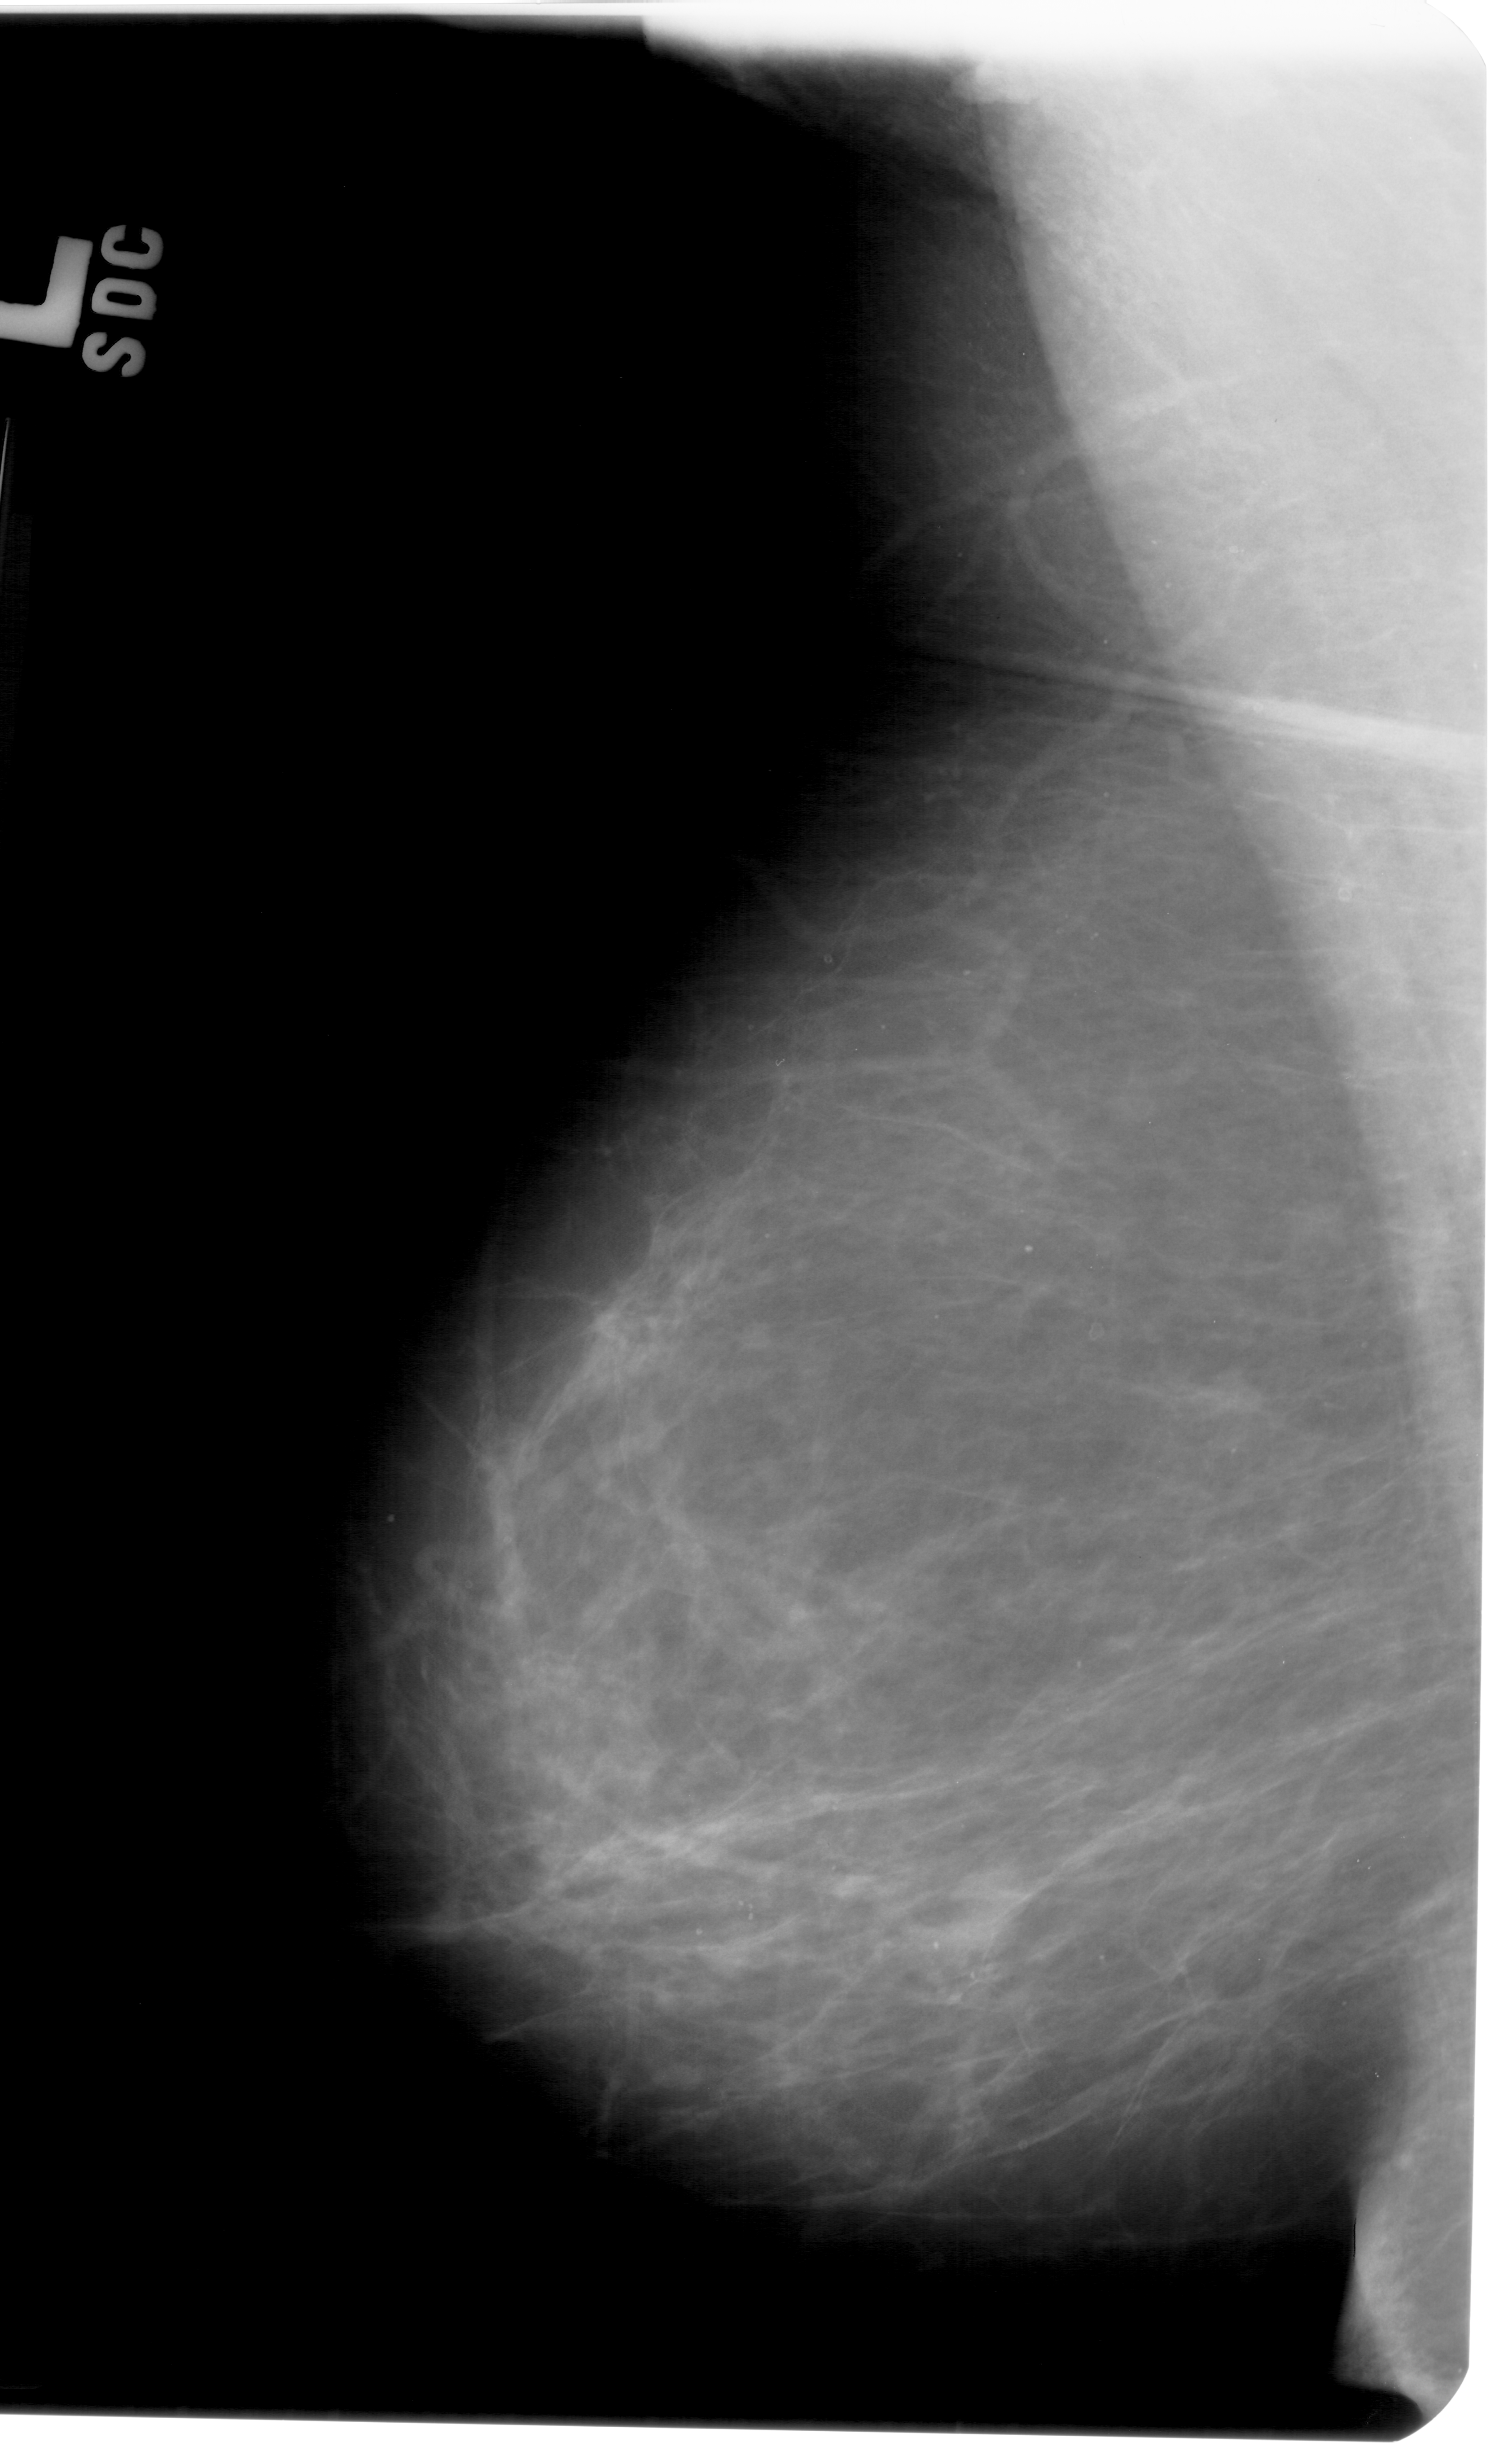
Mammogram (digitized film); left breast; MLO view; BI-RADS breast density category 3 (scale 1–4).
Mass, shape oval, margins circumscribed / obscured; BI-RADS assessment category 4; subtlety rating 4 on a 1 (subtle) to 5 (obvious) scale; pathology (as recorded): benign.